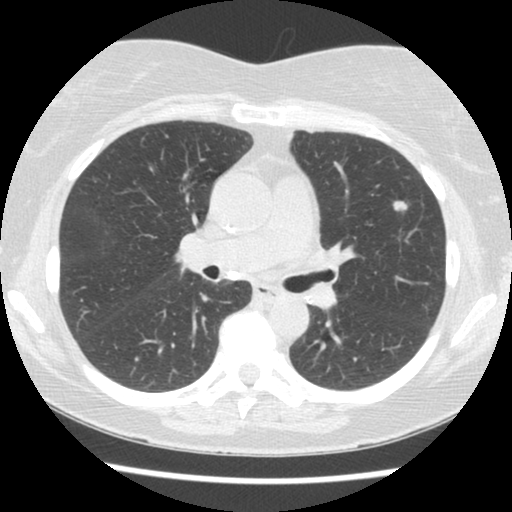
Axial slice from a low-dose chest CT screening exam; second annual screen; lung window (W 1500 / L -600 HU); 2.5 mm slice thickness. Female participant, aged 60 years at enrolment. Current smoker at enrolment.
• Expert reader's lesion annotation, box from (x=377, y=193) to (x=420, y=226) px.
• The screening reader recorded 3 non-calcified nodules or masses ≥4 mm on this exam; which of them this box marks is not recorded.